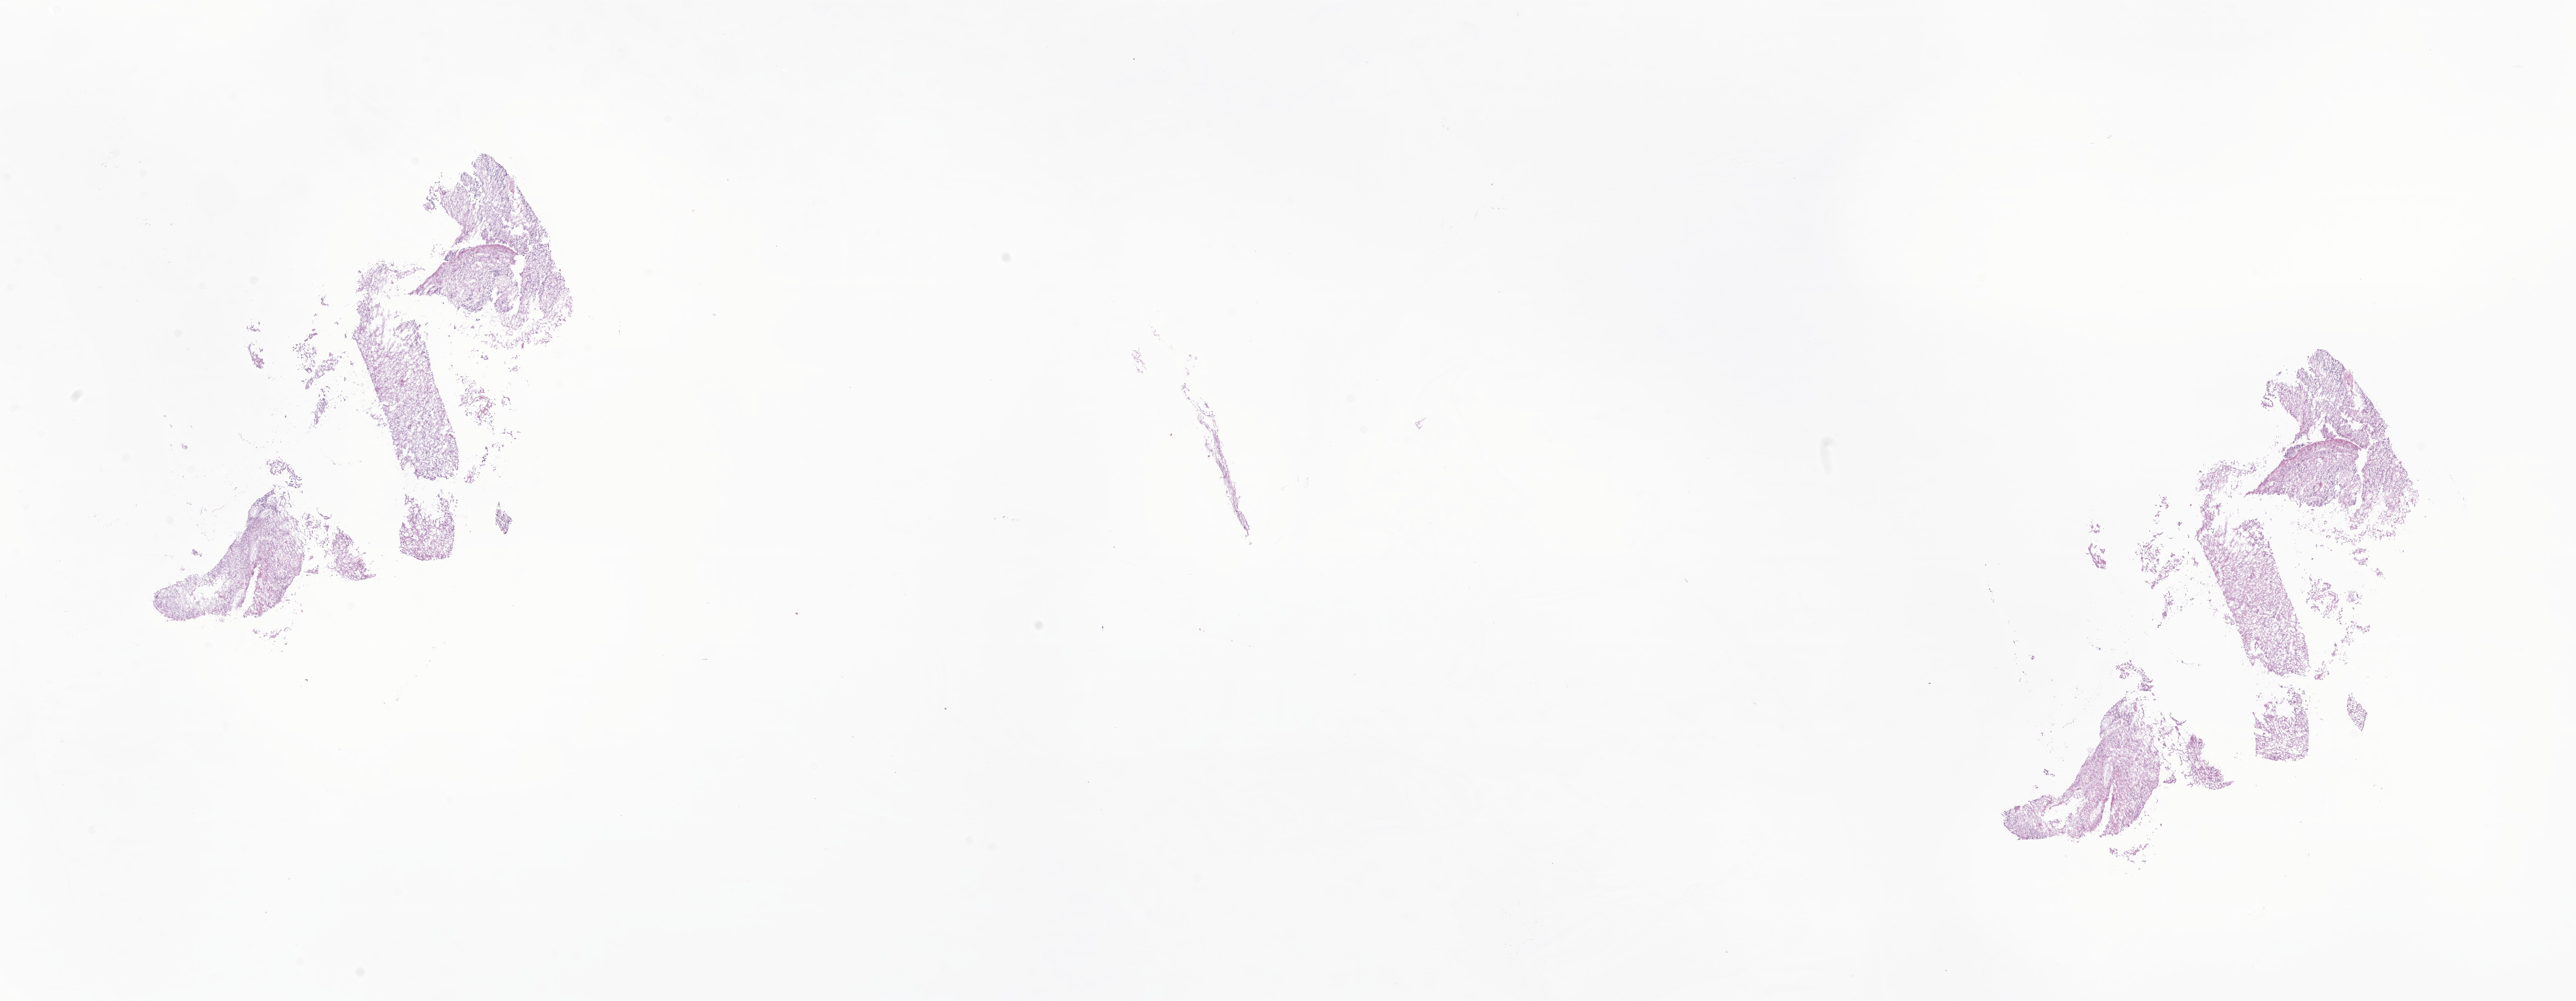
Digitized hematoxylin and eosin (H&E)-stained section of tumor tissue from the brain, low-resolution overview of the scanned area, about 30.7 x 11.9 mm, frozen section (OCT-embedded). Female patient, age 439 days (about 1.2 years).
Diagnosis (ICD-O-3 morphology term): Ependymoma, NOS.